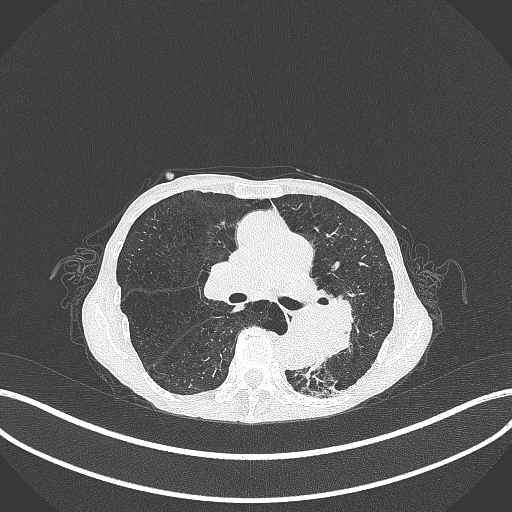
Chest CT, one axial slice. Slice 161 of 347 in the series (ordered by position). Reconstruction kernel B70f. 120 kVp. Lung window (W 1500 / L -600 HU). 1 mm slice thickness. 512 × 512 image matrix, field of view 400 × 400 mm. Female patient, age 70 years. From the clinical record (not read from this slice): clinical TNM (as recorded): T3 N0 M0.
Structures marked on this image (bounding box drawn by a radiologist):
- lung tumour (recorded histology: small cell carcinoma): bounding box [x1, y1, x2, y2] px = [279, 299, 362, 369]